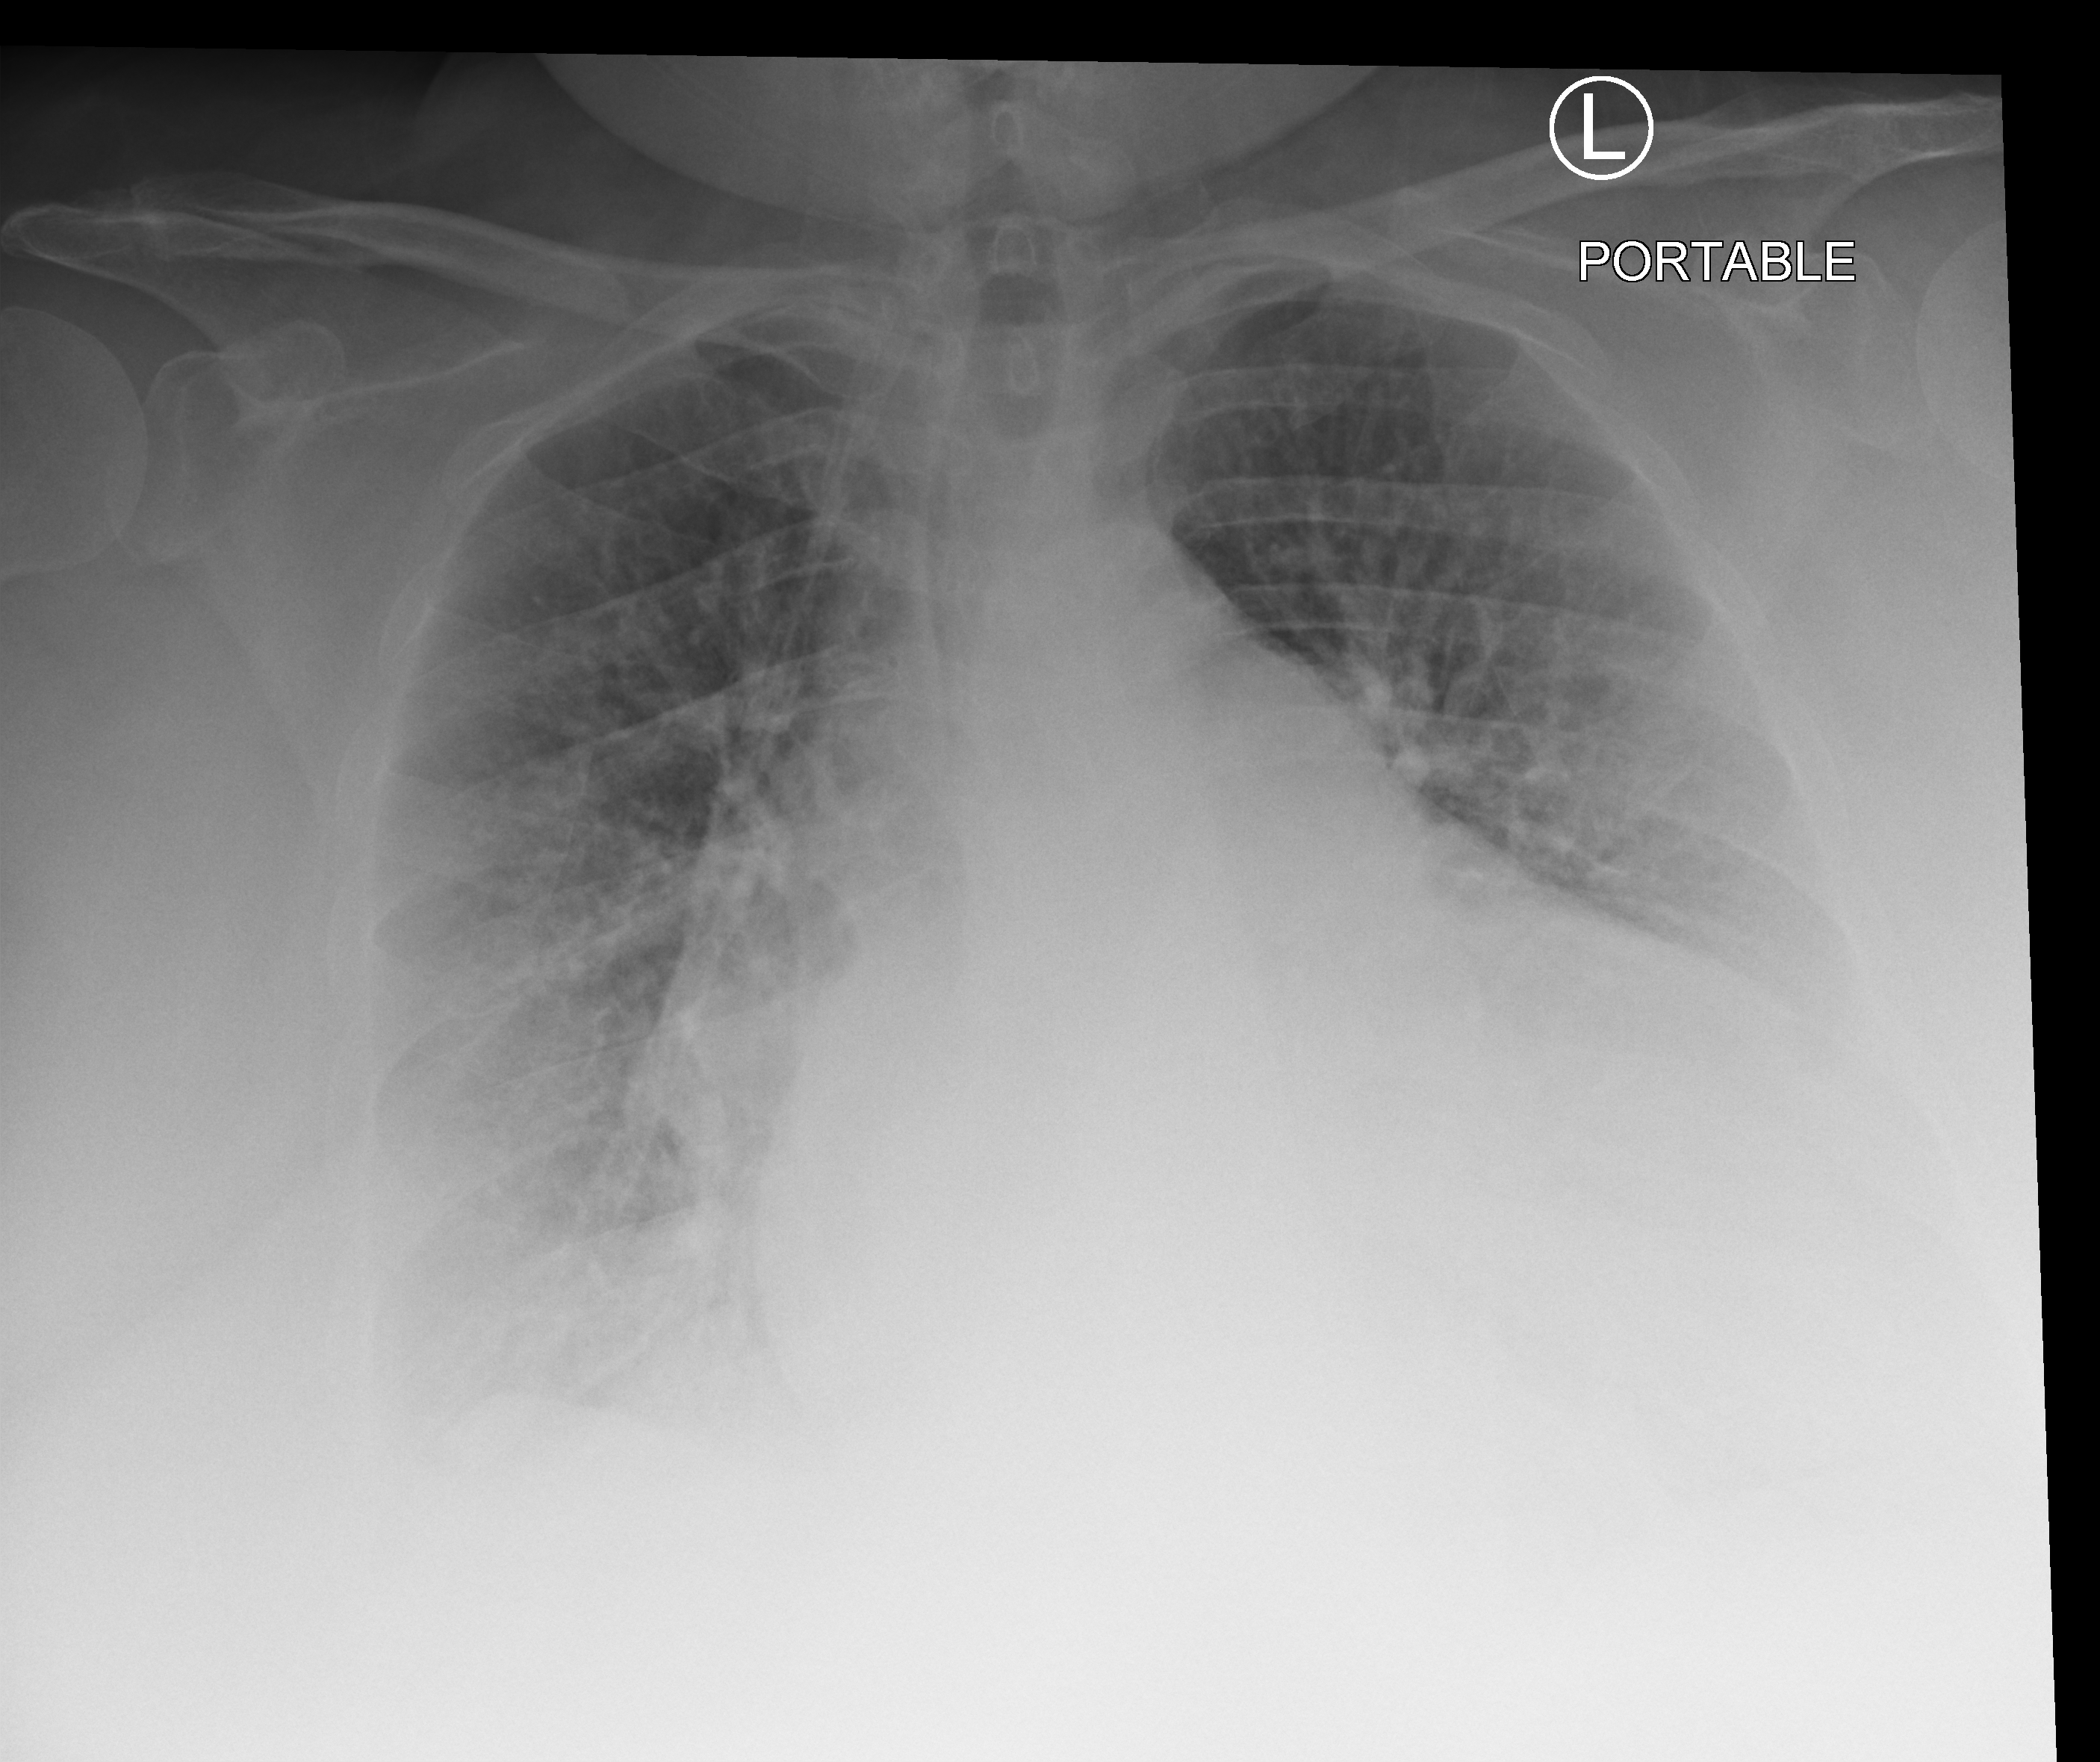
Portable chest radiograph. Patient hospitalised with COVID-19; female, aged 60–74 years.
Admission-level facts for this patient (not findings on this image; timing relative to this image not recorded): chronic kidney disease (admission record): no.